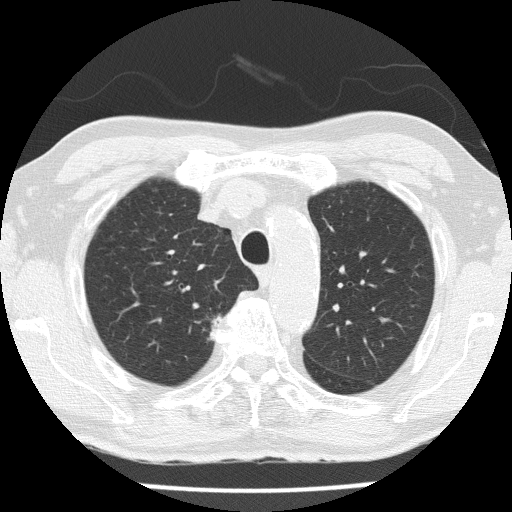
Low-dose screening chest CT, axial slice; third screening round (two years after baseline); lung window (W 1500 / L -600 HU); 2 mm slice thickness; lung (sharp) reconstruction kernel (FC51); slice 40 of 153 in the series; 512 × 512 image matrix. Male participant, aged 72 years at enrolment. Current smoker at enrolment.
- Expert reader's lesion annotation, bounding box <187,300,236,348> (left, top, right, bottom; pixels).
- Reader record for this screening exam (exam-level; its link to the box is not recorded): non-calcified nodule or mass ≥4 mm, right upper lobe, 14 × 14 mm, spiculated (stellate) margins, soft tissue attenuation, pre-existing on the prior screen: yes; interval growth: yes.
- Later outcome: lung cancer diagnosed 67 days after this screen — squamous cell carcinoma, NOS, right upper lobe, moderately differentiated (G2), stage IIA (AJCC 6th edition), 25 mm at pathology.